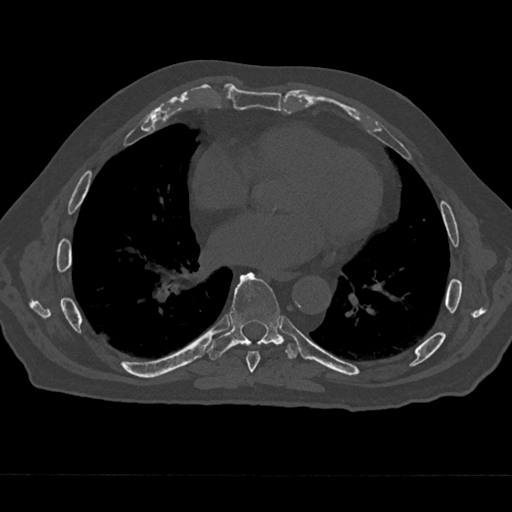
CT including the spine, one axial slice; slice 337 of 797 in the series (ordered by position); reconstruction kernel Br40s/3; bone window (W 1800 / L 400 HU); 512 × 512 image matrix. Patient: male, 75 years. Case-level facts recorded for this patient, not image findings: primary cancer: renal.
Structures marked on this image (semi-automatic segmentation, software-assisted and operator-edited):
- T7 vertebra: bounding box (x1, y1, x2, y2) in pixels: (246, 351, 260, 376)
- T8 vertebra: (207, 272, 299, 360)